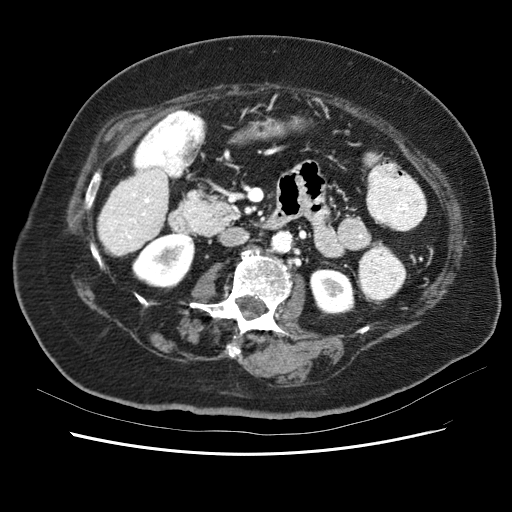
Contrast-enhanced abdominal CT (liver protocol), one axial slice. Slice 14 of 62 in the series (ordered by position). 120 kVp. Soft-tissue window (W 400 / L 40 HU). 2.5 mm slice thickness. 512 × 512 image matrix, field of view 340 × 340 mm. From the clinical record (not read from this slice): diagnosis: hepatocellular carcinoma (patient treated with transarterial chemoembolisation; whether this scan precedes or follows treatment is not stated here); TNM stage (as recorded): Stage-I; Child-Pugh class: B.
Annotated regions visible in this slice (semi-automatically segmented with operator editing):
- liver parenchyma outside the tumour (the mass and vessels are separate outlines, so this box may not span the whole liver): bounding box [x1, y1, x2, y2] px = [96, 153, 170, 260]
- liver vessels: [99, 156, 163, 250]